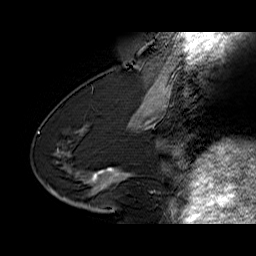
Breast MRI (dynamic contrast-enhanced), one sagittal slice; position 30 of 60 along the scan axis; dynamic contrast-enhanced series, time point 2 of 6 at this slice position (early post-contrast); 1.5 T; TE 6.4 ms, TR 32.9 ms; 256 × 256 image matrix. Female patient. From the clinical record (not read from this slice): setting: breast cancer imaged before/during neoadjuvant chemotherapy; receptor status: HR-positive, HER2-negative.
Annotated regions visible in this slice (semi-automatic segmentation, software-assisted and operator-edited):
- analysis volume of interest (the breast-tissue region the enhancement analysis was run in; not a lesion): bounding box (x1, y1, x2, y2) in pixels: (68, 154, 129, 203)
- tumour enhancement mask (voxels above the 100 % enhancement threshold inside the analysis volume of interest): (90, 169, 128, 184)